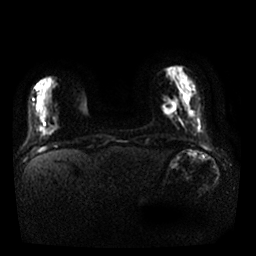
Breast MRI, one axial slice; slice 5 of 25 in the series (ordered by position); diffusion-weighted series; image 2 of 4 stored at this slice position (different b-values; order by instance number); 1.5 T; 256 × 256 image matrix, field of view 340 × 340 mm. Female patient.
Structures marked on this image (manually delineated by an expert):
- tumour on diffusion-weighted imaging: box from (x=163, y=98) to (x=176, y=114) px